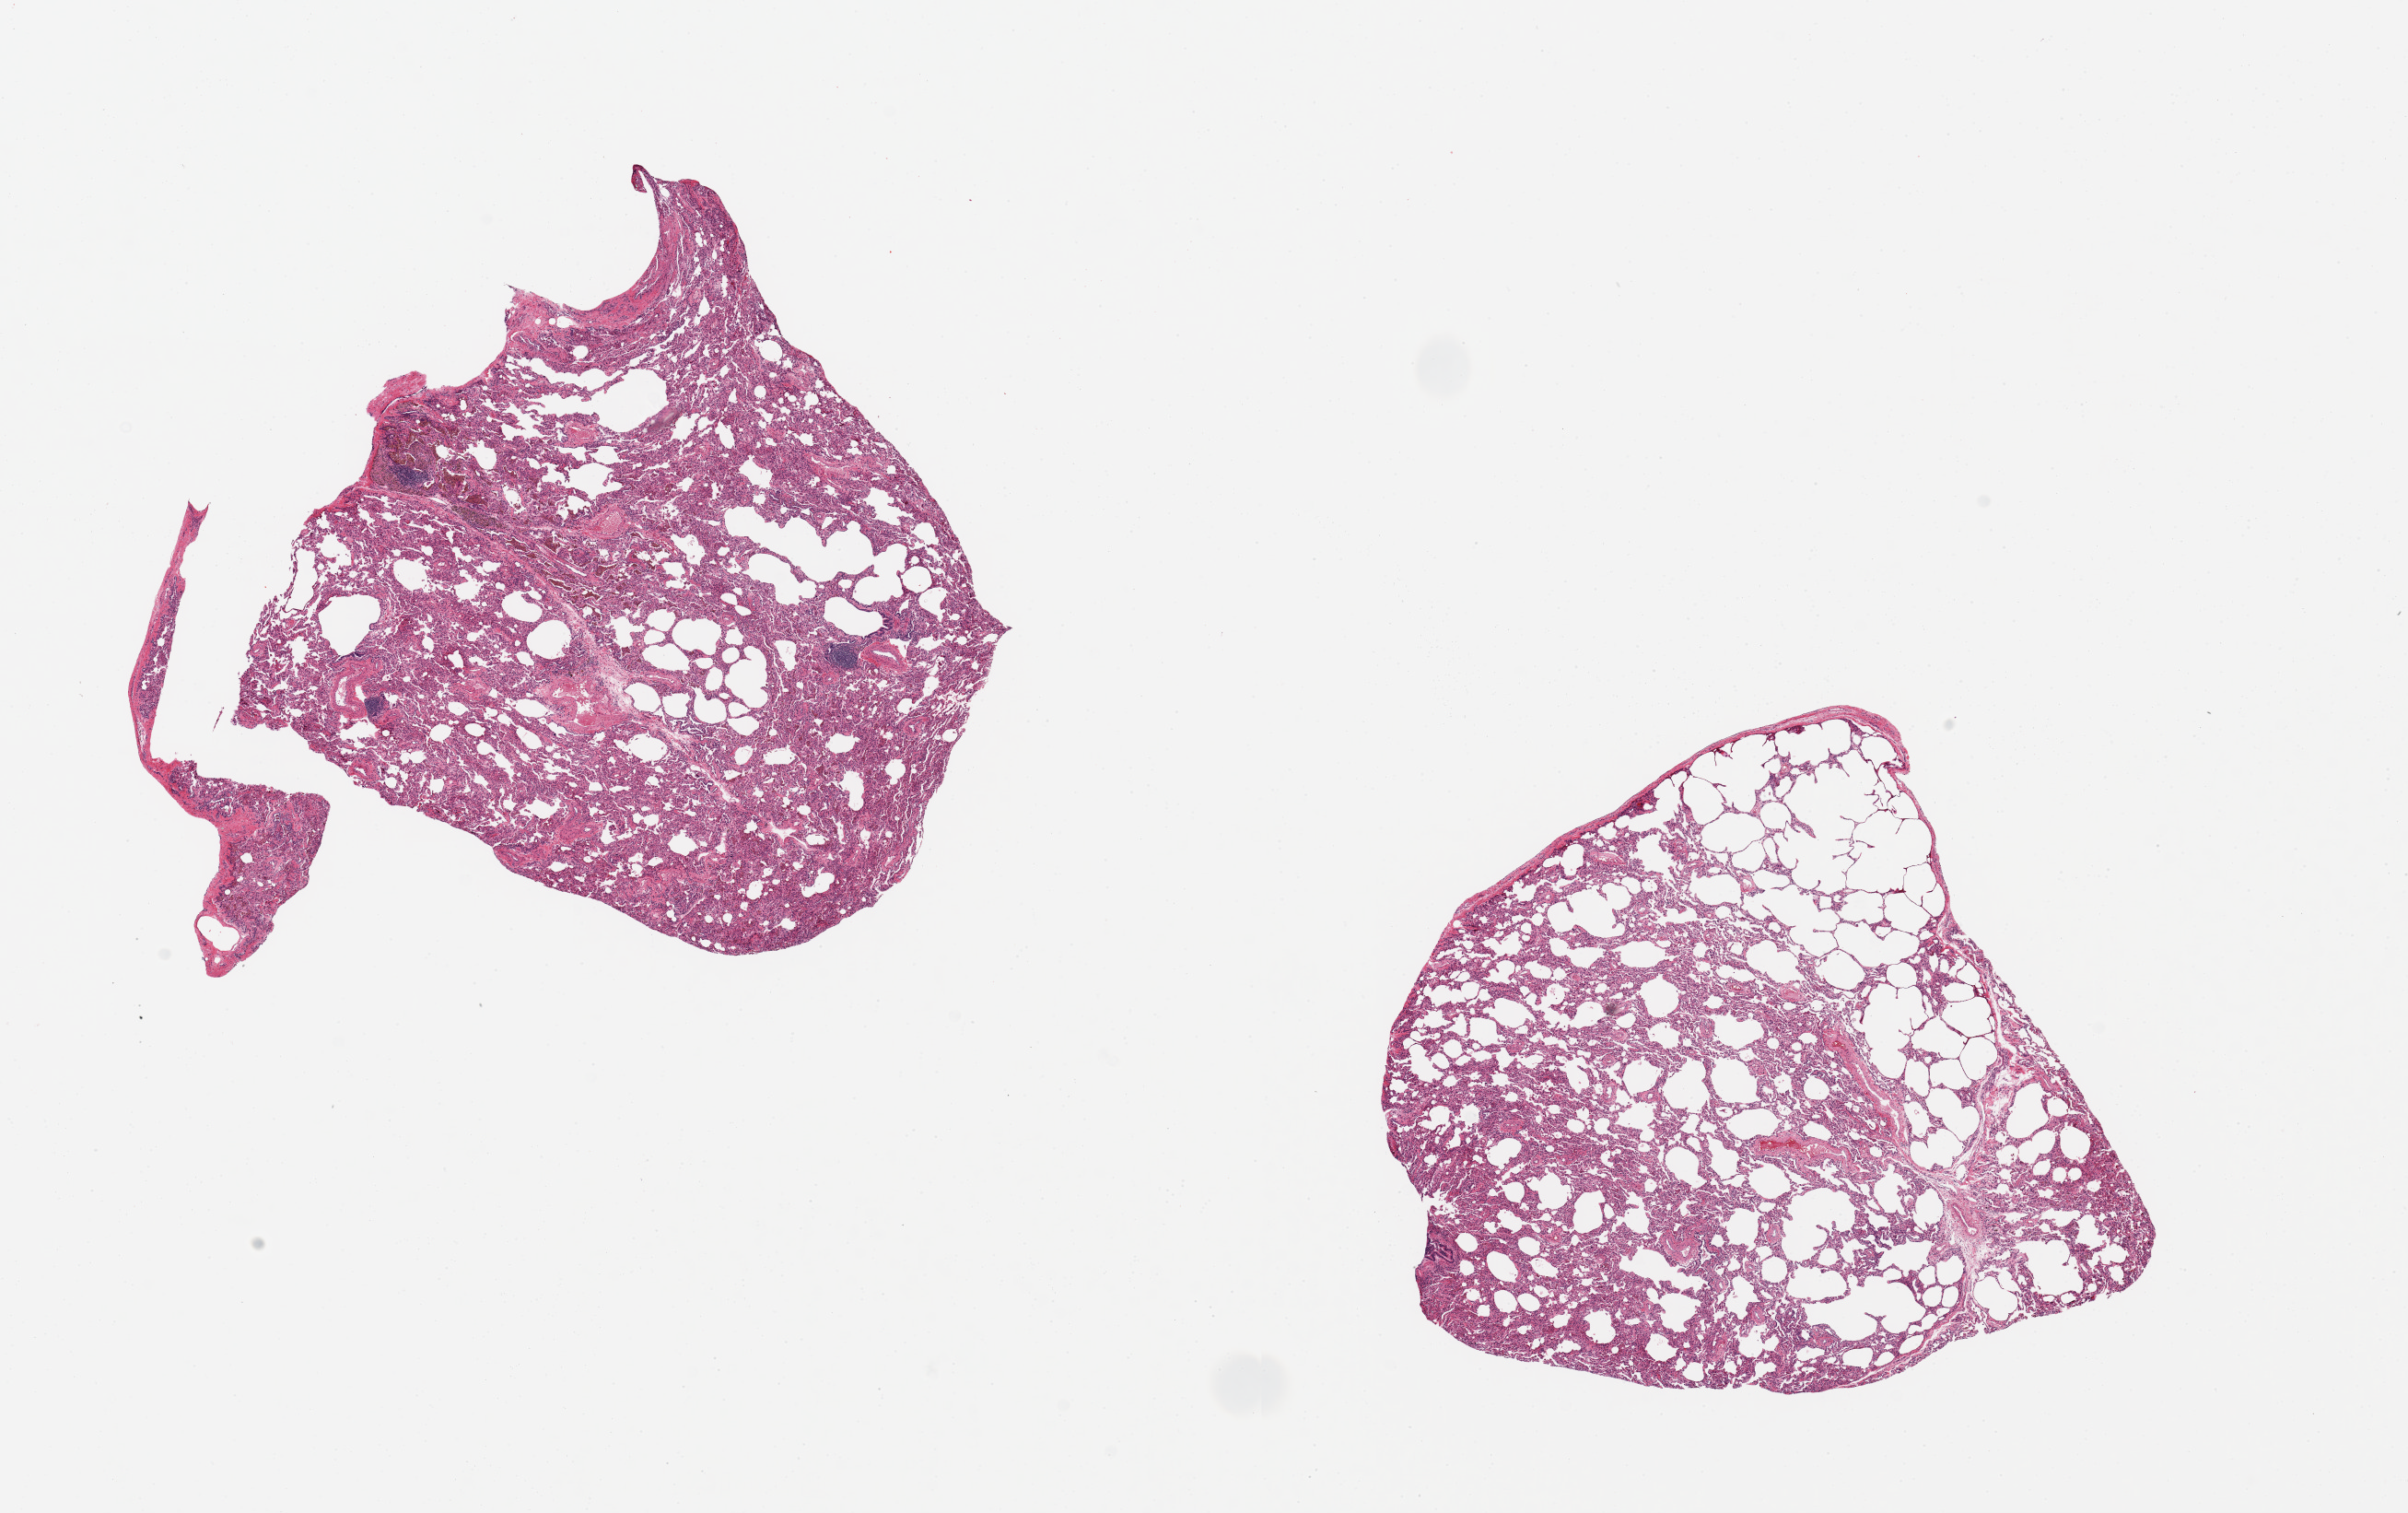
H&E whole-slide image — low-resolution overview of the scanned area, about 20.7 x 13.0 mm (acquisition: 20x scan). PAXgene-fixed, paraffin-embedded tissue. Target tissue: lung. Donor tissue sample. Male donor.
Reviewer comment on this tissue sample: 2 pieces, 6x6 & 7x6mm; heart failure cells, mild patchy pneumonia.